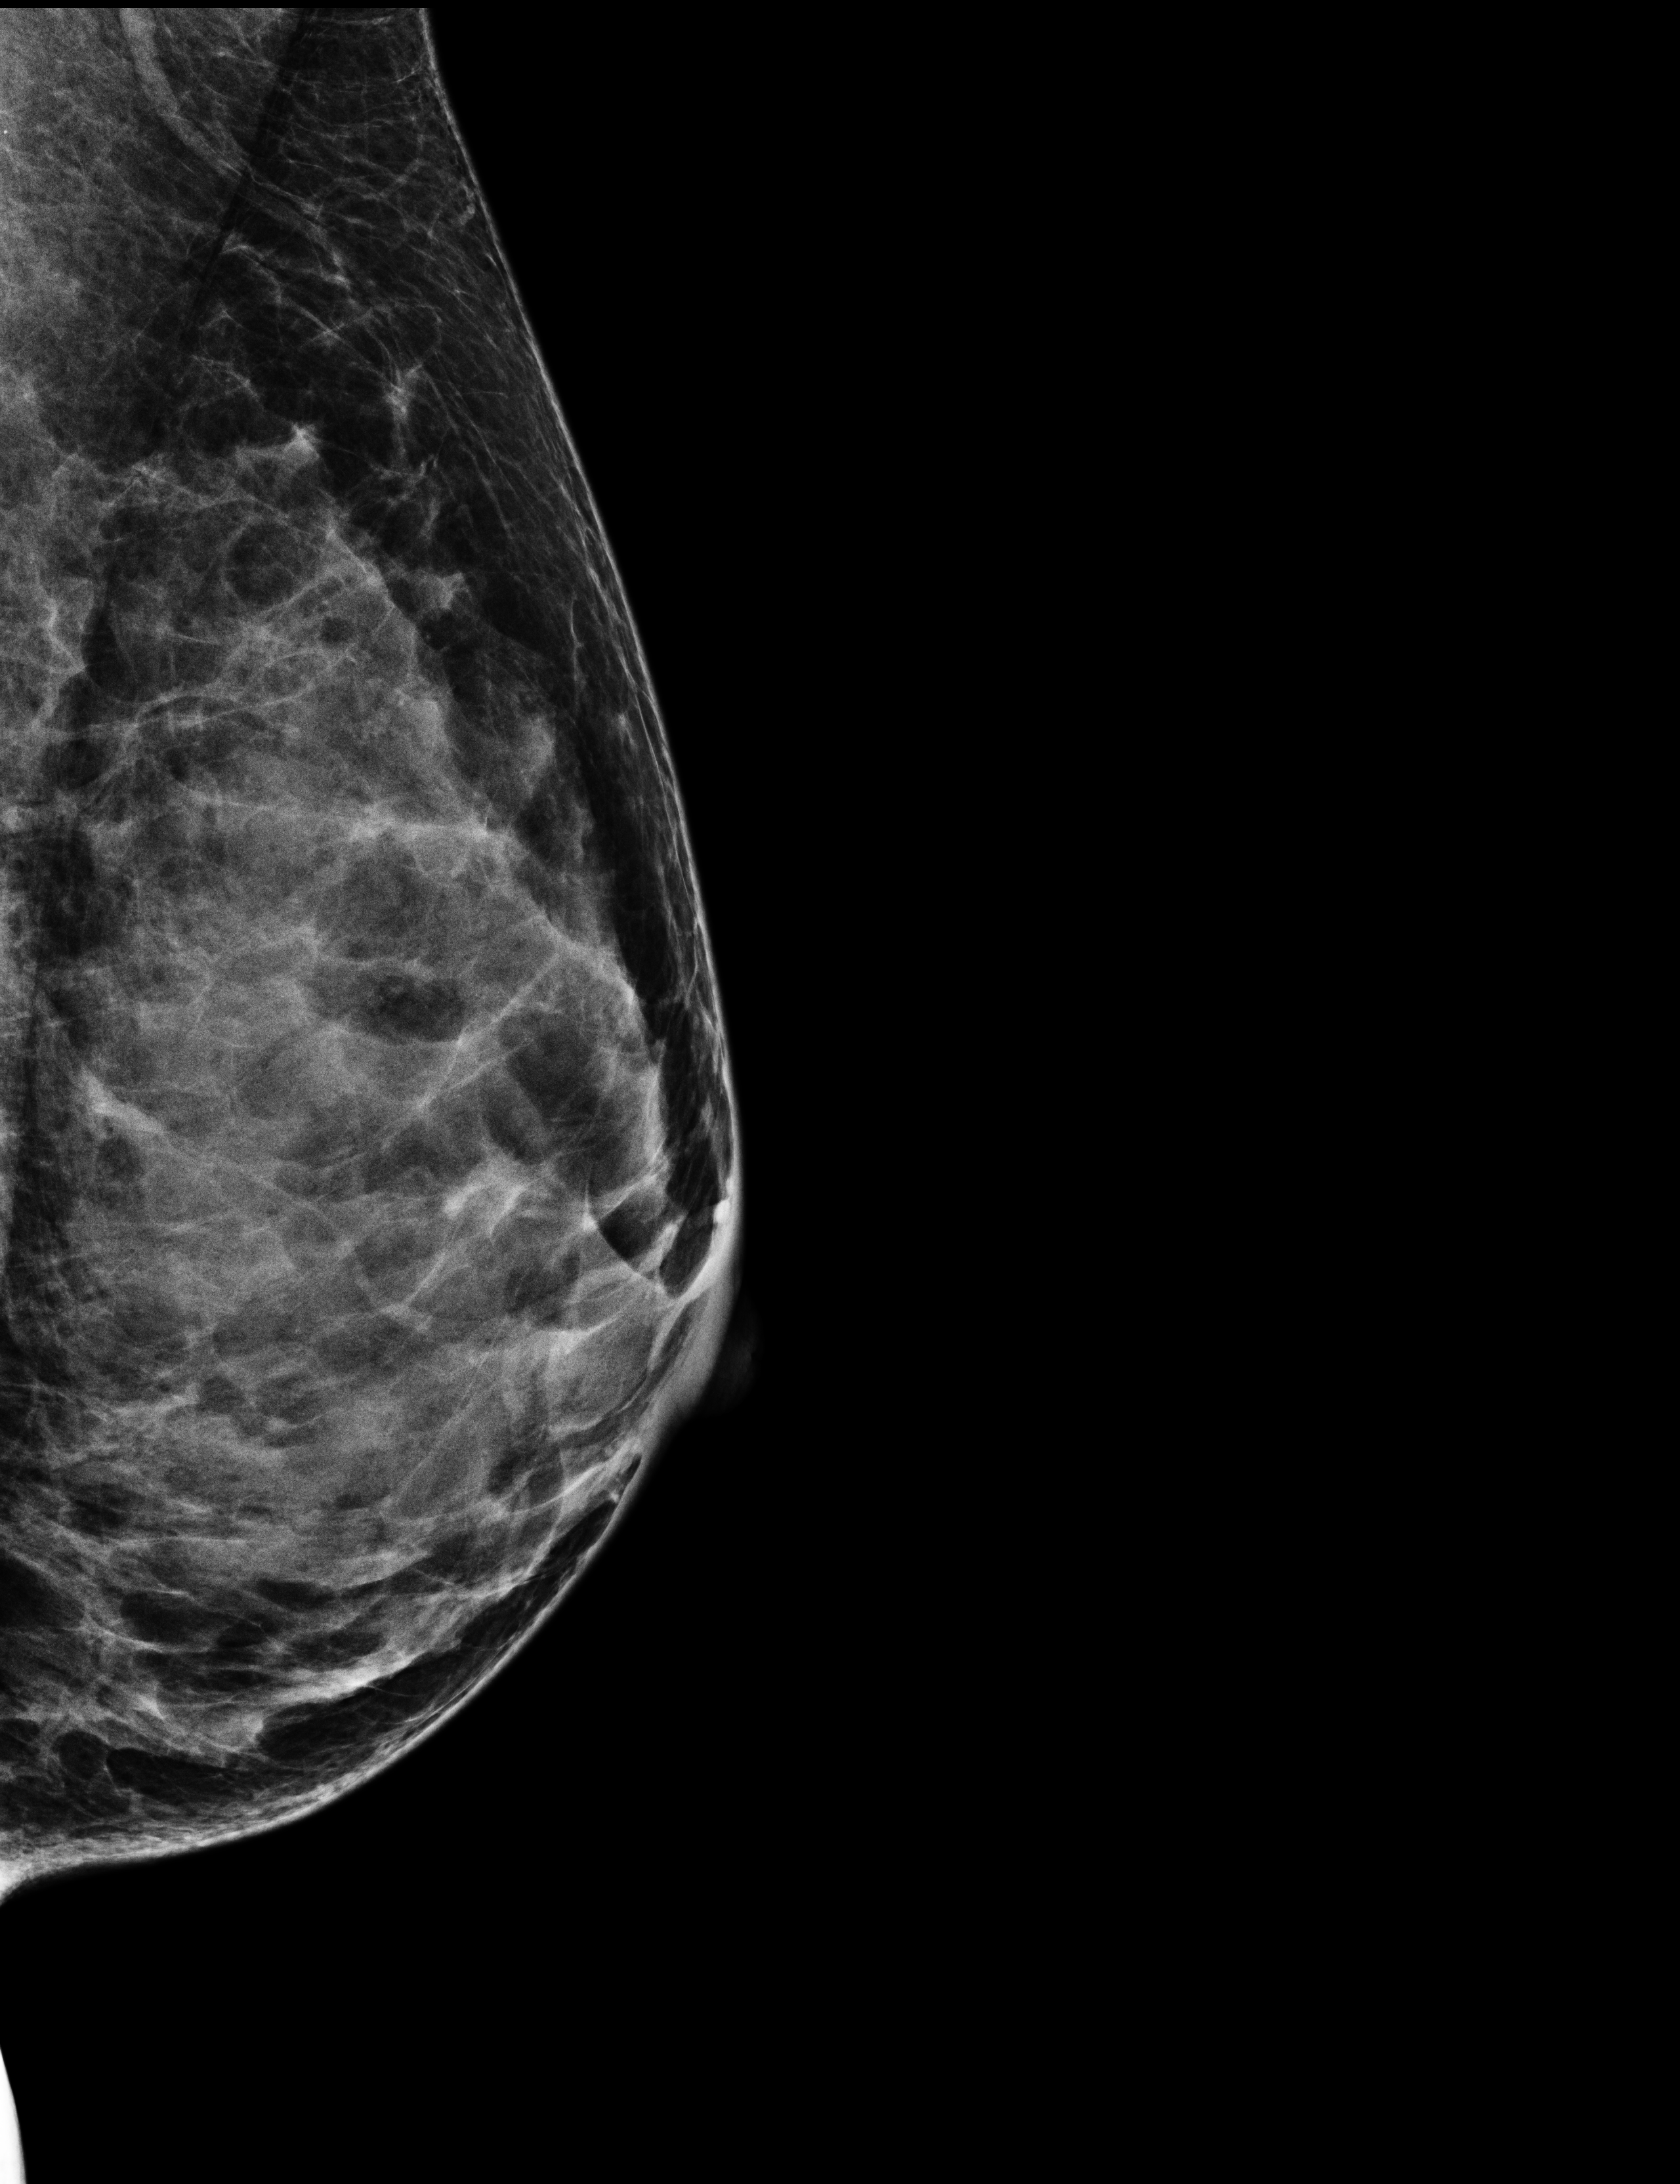
Screening examination. Female patient, age 43 years.
Image type: full-field digital mammogram. Breast: left. Projection: mediolateral oblique (MLO) view.